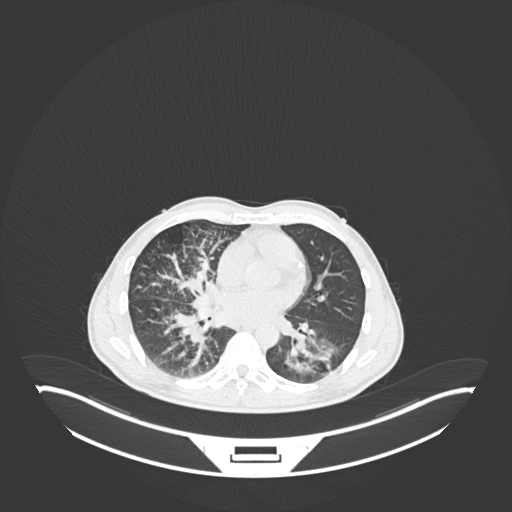
Chest CT, one axial slice. Slice 110 of 237 in the series (ordered by position). 120 kVp. Lung window (W 1500 / L -600 HU). 512 × 512 image matrix, field of view 500 × 500 mm. Male patient, age 49 years. From the clinical record (not read from this slice): clinical TNM (as recorded): T2b N1 M0.
Outlined on this slice (rectangle marked by the reading radiologist):
- lung tumour (recorded histology: adenocarcinoma): bounding box (x1, y1, x2, y2) in pixels: (285, 326, 340, 379)